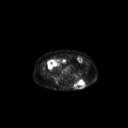
FDG PET of an extremity soft-tissue mass (from a PET/CT study), one axial slice. Position 82 of 267 along the scan axis. 128 × 128 image matrix. Male patient, age 69 years. Case-level facts recorded for this patient, not image findings: histological type: leiomyosarcoma; grade: intermediate; site of the primary tumour: left pelvis.
Annotated regions visible in this slice (expert contour drawn on MRI and transferred to this co-registered scan by the dataset authors):
- gross tumour volume (mass): bounding box [x1, y1, x2, y2] px = [73, 78, 86, 89]